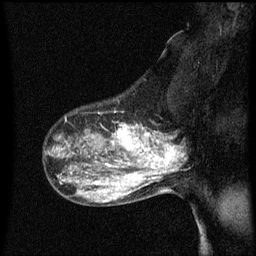
Breast MRI (dynamic contrast-enhanced), one sagittal slice; position 43 of 60 along the scan axis; dynamic contrast-enhanced series, image 2 of 3 at this slice position (ordered by acquisition); 1.5 T; TE 4.2 ms, TR 8.4 ms; 2 mm slice thickness; 256 × 256 image matrix, field of view 200 × 200 mm. Female patient, age 50 years.
Structures marked on this image (semi-automatically segmented with operator editing):
- analysis volume of interest (the breast-tissue region the enhancement analysis was run in; not a lesion): bounding box [x1, y1, x2, y2] px = [100, 114, 153, 171]
- tumour enhancement mask (voxels above the 70 % enhancement threshold inside the analysis volume of interest): [105, 124, 153, 169]